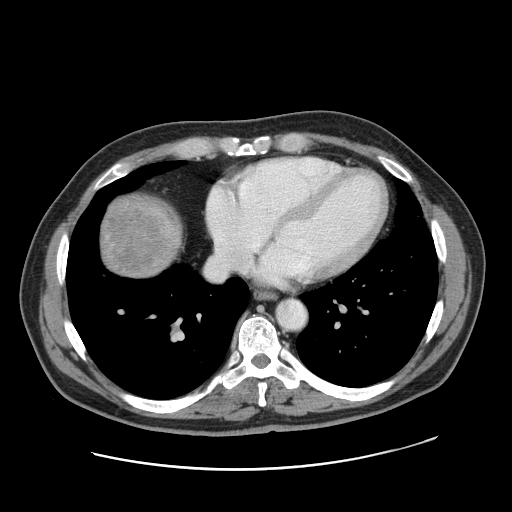
Contrast-enhanced abdominal CT, one axial slice; position 160 of 178 along the scan axis; 120 kVp; intravenous contrast given; soft-tissue window (W 400 / L 40 HU); 2.5 mm slice thickness; 512 × 512 image matrix, field of view 403 × 403 mm. Male patient, age 63 years. Case-level facts recorded for this patient, not image findings: diagnosis: colorectal cancer liver metastases, imaged before liver resection; multiple liver metastases: yes; largest metastasis: 8 cm; disease in both lobes: yes.
Structures marked on this image (outlined manually by an expert reader):
- liver: bounding box <99,197,182,279> (left, top, right, bottom; pixels)
- liver metastasis: <104,196,164,276>